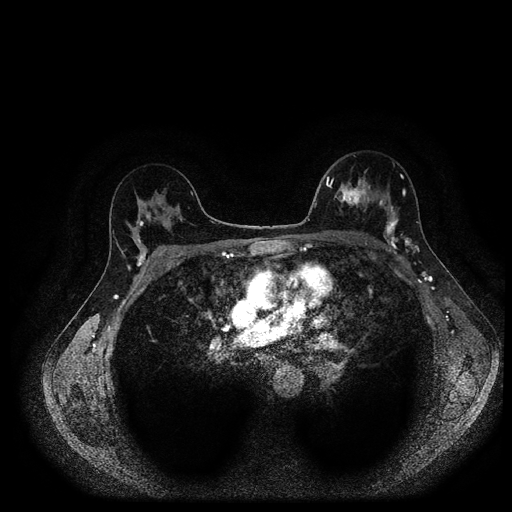
Breast MRI (dynamic contrast-enhanced, multi-phase), one axial slice. Slice 65 of 116 in the series (ordered by position). Dynamic contrast-enhanced series, time point 2 of 5 at this slice position (early post-contrast). 1.5 T. TE 2.7 ms, TR 5.4 ms. 2 mm slice thickness. 512 × 512 image matrix, field of view 340 × 340 mm. Patient: female, 40 years.
Outlined on this slice (semi-automatic segmentation, software-assisted and operator-edited):
- breast lesion (labelled 'tumour' in the annotation; benign lesions carry a separate 'benign' label): box from (x=333, y=177) to (x=372, y=210) px